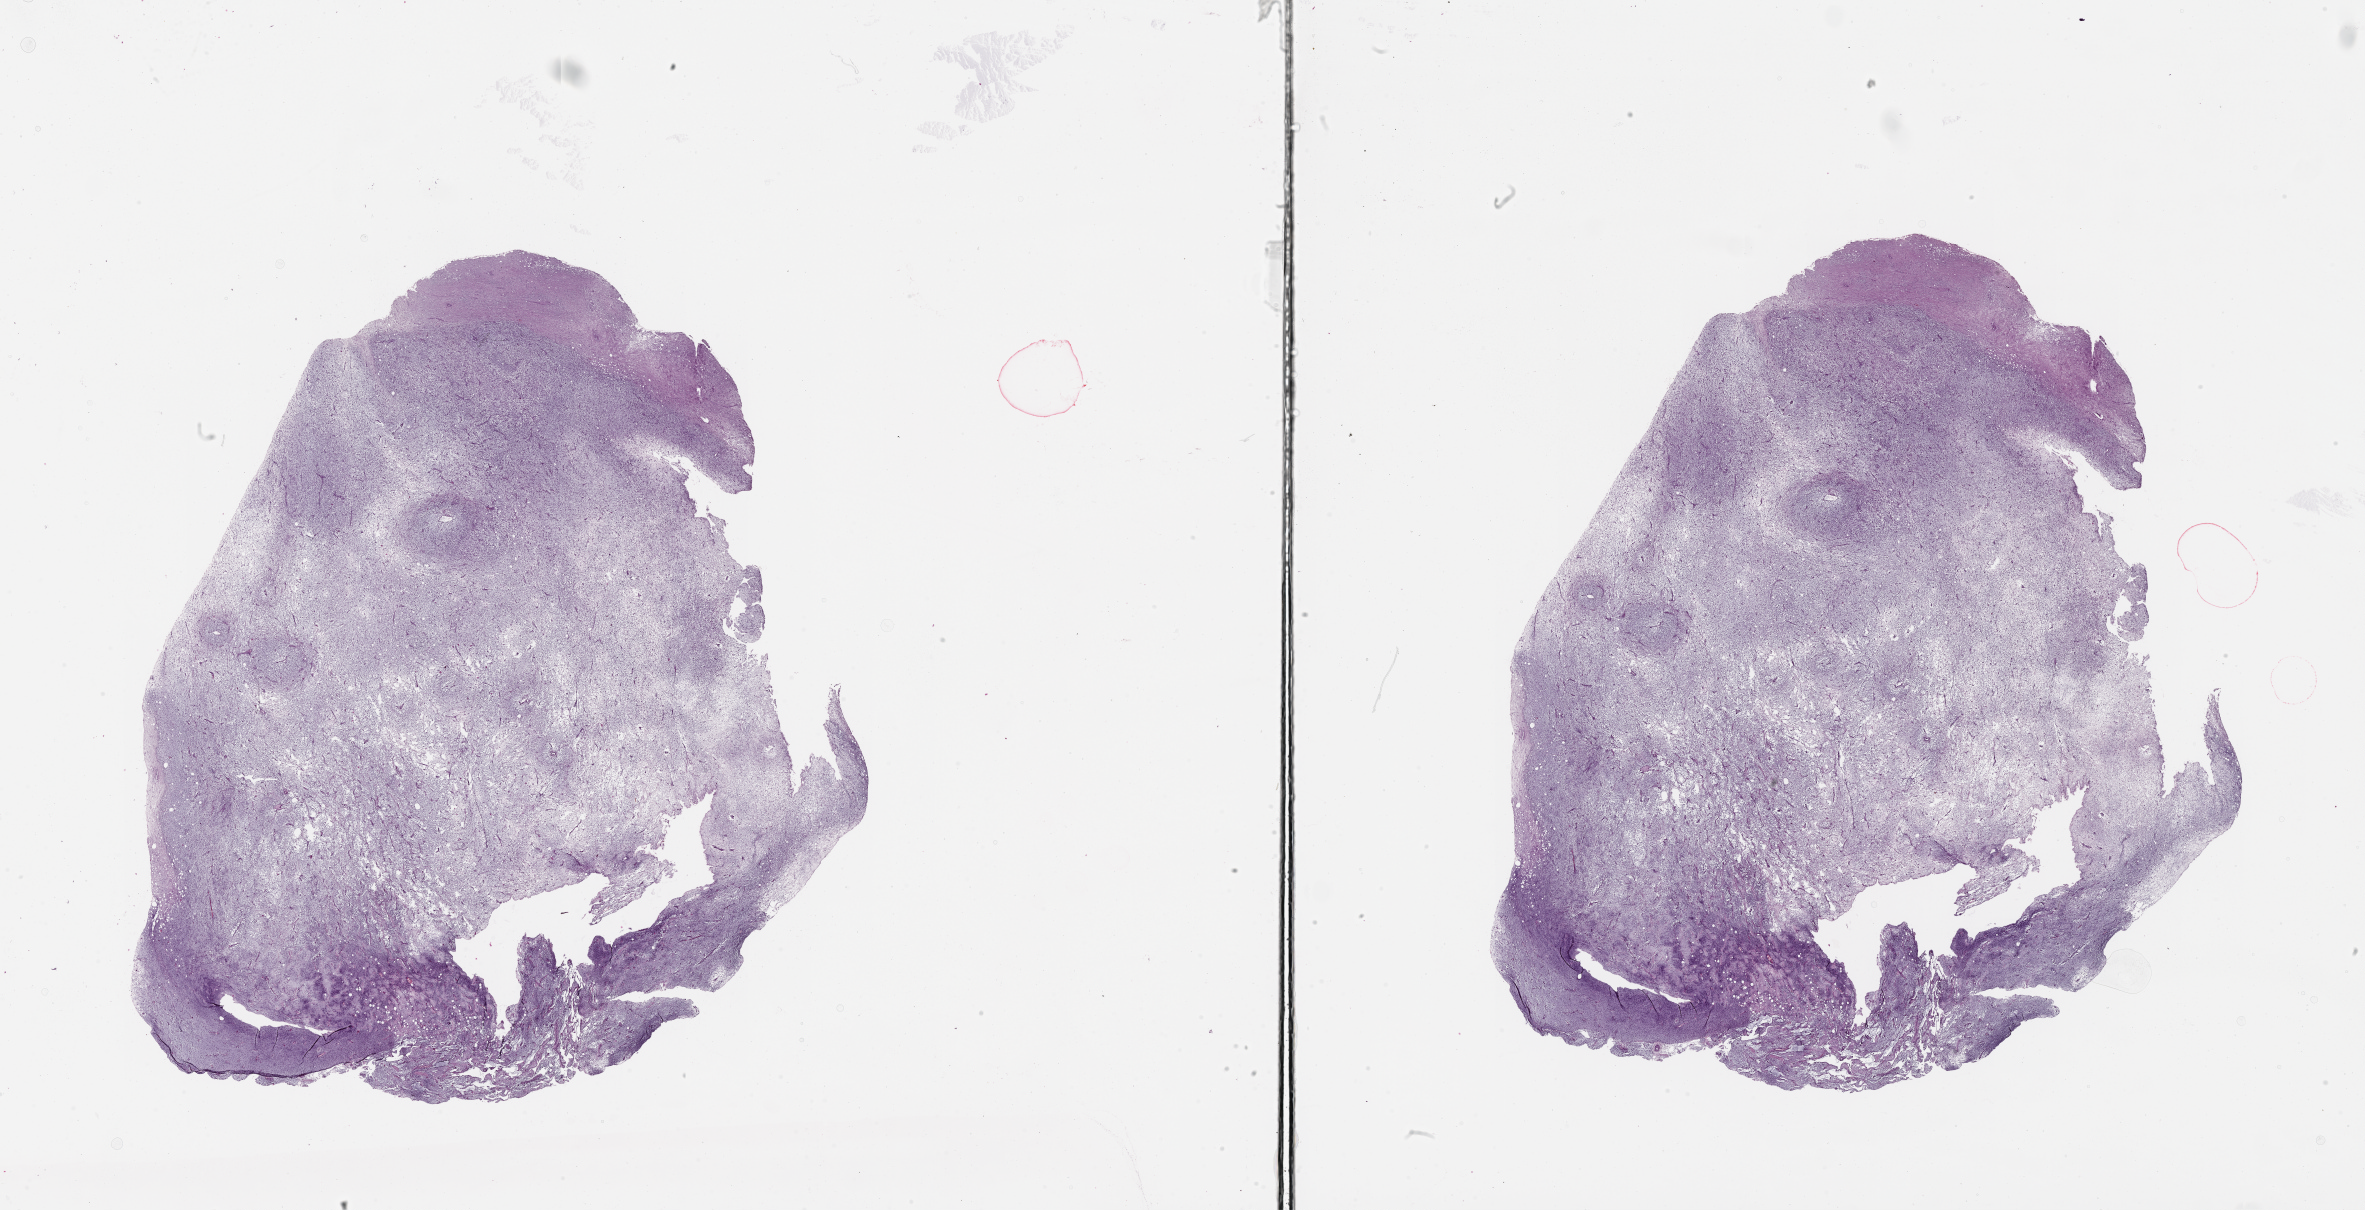
Whole-slide histology image, Hematoxylin and eosin (H&E) stained, shown as a low-resolution overview of the whole scanned area (about 38.1 x 19.5 mm, from a 20x scan). Tumour tissue sample. 78-year-old female patient.
Primary tumour site (as recorded): lower extremity. Patient diagnosis (cohort enrolment): sarcoma (site not recorded at cohort level).